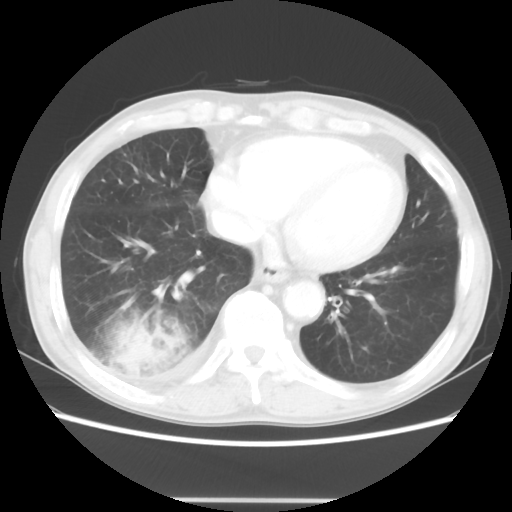
Chest CT, one axial slice; position 12 of 48 along the scan axis; reconstruction kernel STANDARD; lung window (W 1500 / L -600 HU); 512 × 512 image matrix, field of view 361 × 361 mm. Male patient, age 66 years. Case-level facts recorded for this patient, not image findings: clinical TNM (as recorded): T4 N1 M1; histopathological grade: G3.
Annotated regions visible in this slice (bounding box drawn by a radiologist):
- lung tumour (recorded histology: small cell carcinoma): bounding box <90,307,181,386> (left, top, right, bottom; pixels)